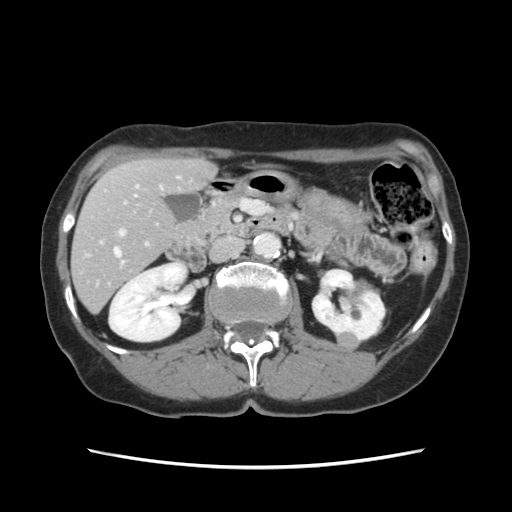
Contrast-enhanced abdominal CT, one axial slice; position 53 of 120 along the scan axis; intravenous contrast given; soft-tissue window (W 400 / L 40 HU); 512 × 512 image matrix. Female patient, age 70 years. From the clinical record (not read from this slice): diagnosis: colorectal cancer liver metastases, imaged before liver resection; multiple liver metastases: no; largest metastasis: 2.5 cm.
Annotated regions visible in this slice (outlined manually by an expert reader):
- hepatic veins: bounding box (x1, y1, x2, y2) in pixels: (114, 248, 121, 256)
- liver: (72, 160, 215, 310)
- planned liver remnant (the part of the liver to remain after resection): (73, 160, 215, 309)
- portal vein (with intrahepatic branches): (100, 177, 180, 246)